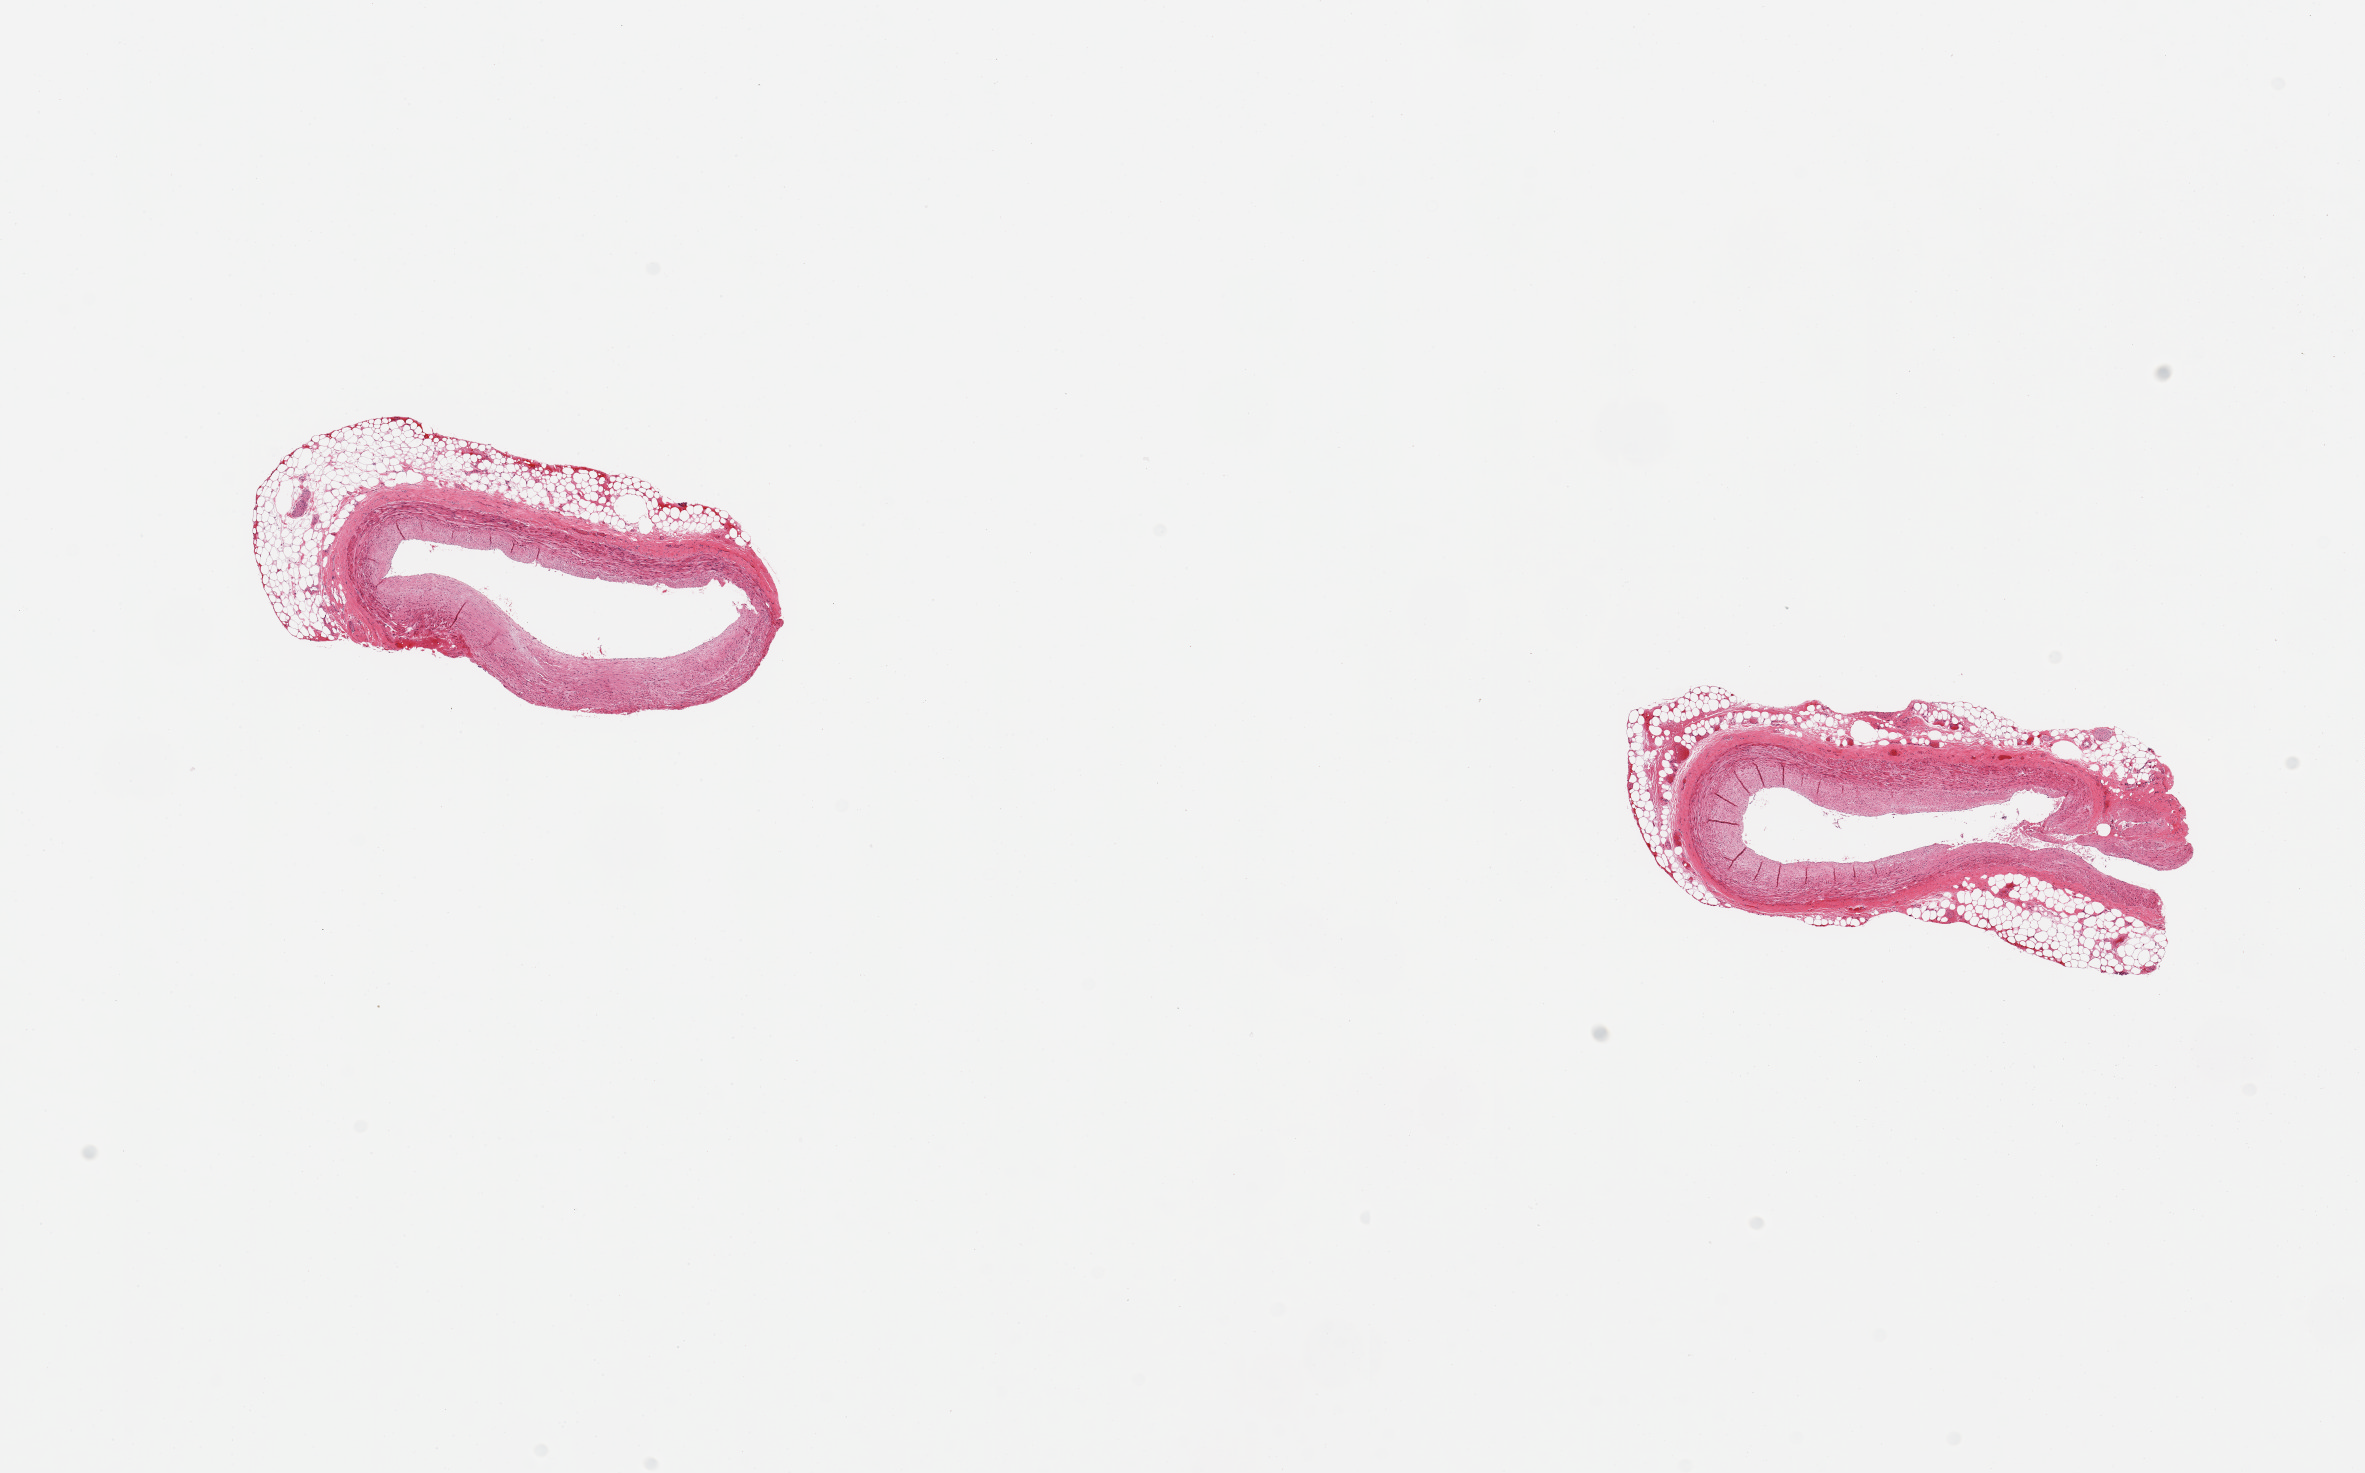
Digitized H&E-stained section, brightfield, a low-resolution overview of the entire scanned area, about 18.7 x 11.6 mm. PAXgene-fixed paraffin-embedded (PFPE) section. Target tissue: coronary artery. Donor tissue sample.
Review note (as recorded): 2 pieces; partial peripheral rim of fat and nerve, up to 30%, atherosclerosis.